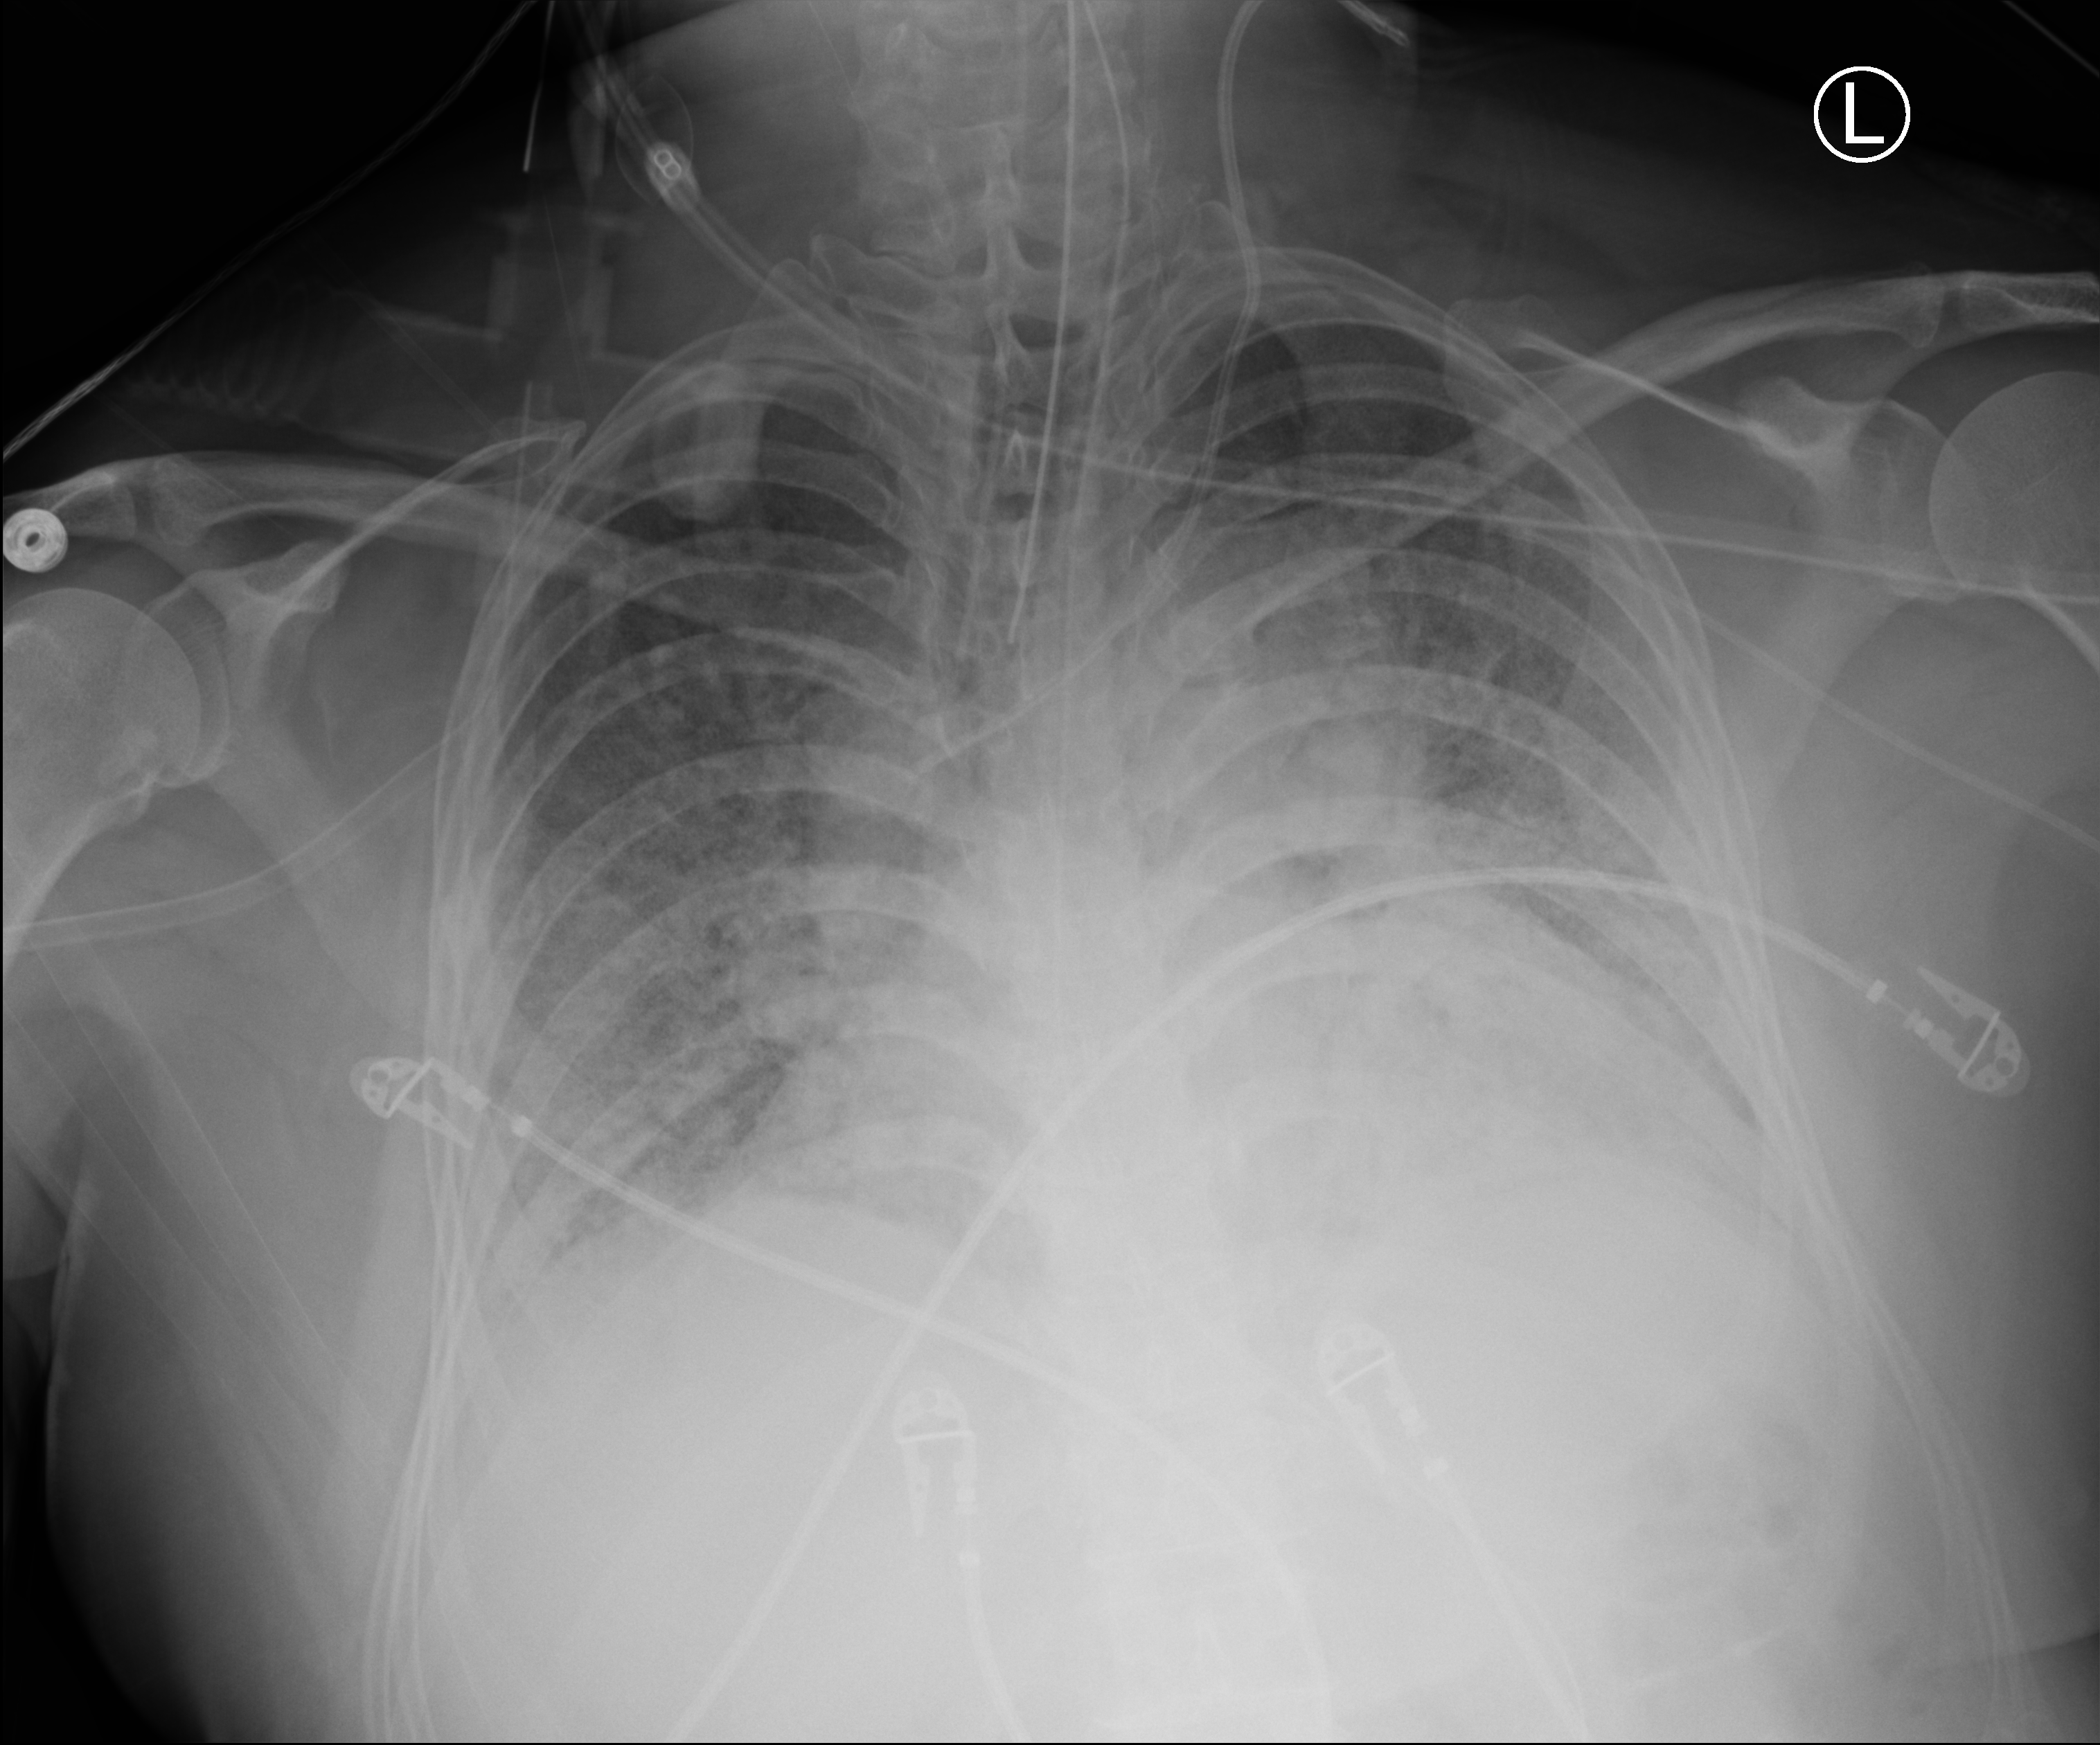
Portable chest radiograph, anteroposterior (AP) projection. Patient hospitalised with COVID-19, aged 18–59 years.
Admission-level facts for this patient (not findings on this image; timing relative to this image not recorded): length of hospital stay: 48 days; admitted to intensive care during this hospital stay: yes.